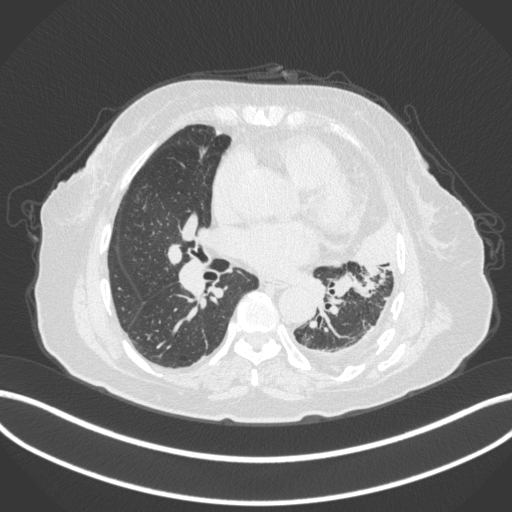
Chest CT, one axial slice; position 178 of 399 along the scan axis; reconstruction kernel B31f; lung window (W 1500 / L -600 HU); 1 mm slice thickness; 512 × 512 image matrix, field of view 400 × 400 mm. Patient: female, 75 years. From the clinical record (not read from this slice): clinical TNM (as recorded): T3 N3 M1.
Structures marked on this image (bounding box drawn by a radiologist):
- lung tumour (recorded histology: adenocarcinoma): bounding box [x1, y1, x2, y2] px = [344, 216, 408, 278]